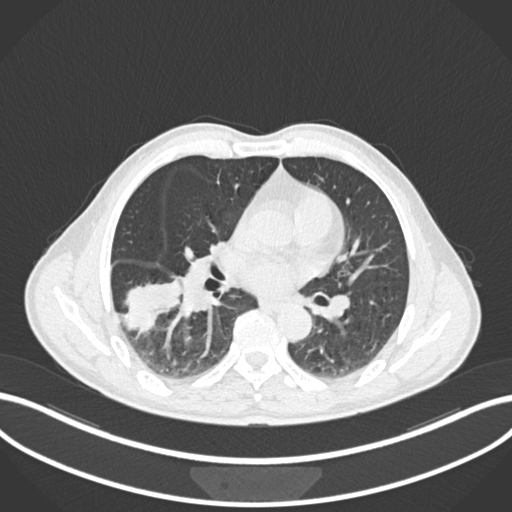
Chest CT, one axial slice. Reconstruction kernel B30f. 120 kVp. Lung window (W 1500 / L -600 HU). 1 mm slice thickness. 512 × 512 image matrix. Patient: male, 58 years. Case-level facts recorded for this patient, not image findings: clinical TNM (as recorded): T3 N0 M0.
Outlined on this slice (rectangle marked by the reading radiologist):
- lung tumour (recorded histology: squamous cell carcinoma): bounding box [x1, y1, x2, y2] px = [123, 273, 183, 342]